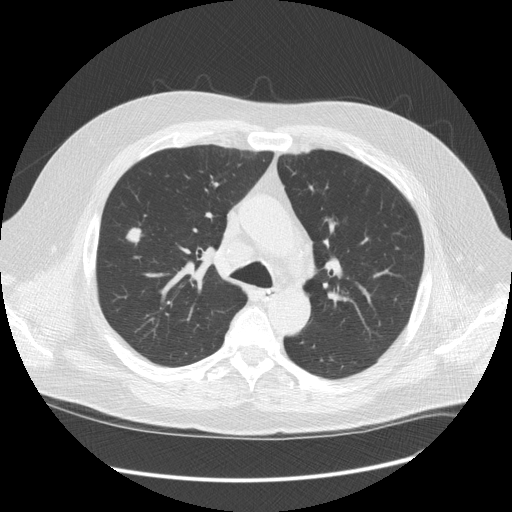
Low-dose screening chest CT, one axial slice. Position 88 of 128 along the scan axis. Reconstruction kernel STANDARD. 120 kVp. Lung window (W 1500 / L -600 HU). 512 × 512 image matrix, field of view 401 × 401 mm.
Outlined on this slice (manually delineated by an expert):
- lesion 1 (tumor, upper lobe of right lung): bounding box [x1, y1, x2, y2] px = [127, 228, 141, 243]